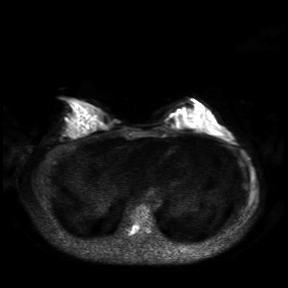
Breast MRI, one axial slice. Position 13 of 30 along the scan axis. Diffusion-weighted series; image 2 of 4 stored at this slice position (different b-values; order by instance number). 3 T. 288 × 288 image matrix, field of view 360 × 360 mm. Female patient.
Outlined on this slice (outlined manually by an expert reader):
- tumour on diffusion-weighted imaging: bounding box <168,110,178,117> (left, top, right, bottom; pixels)